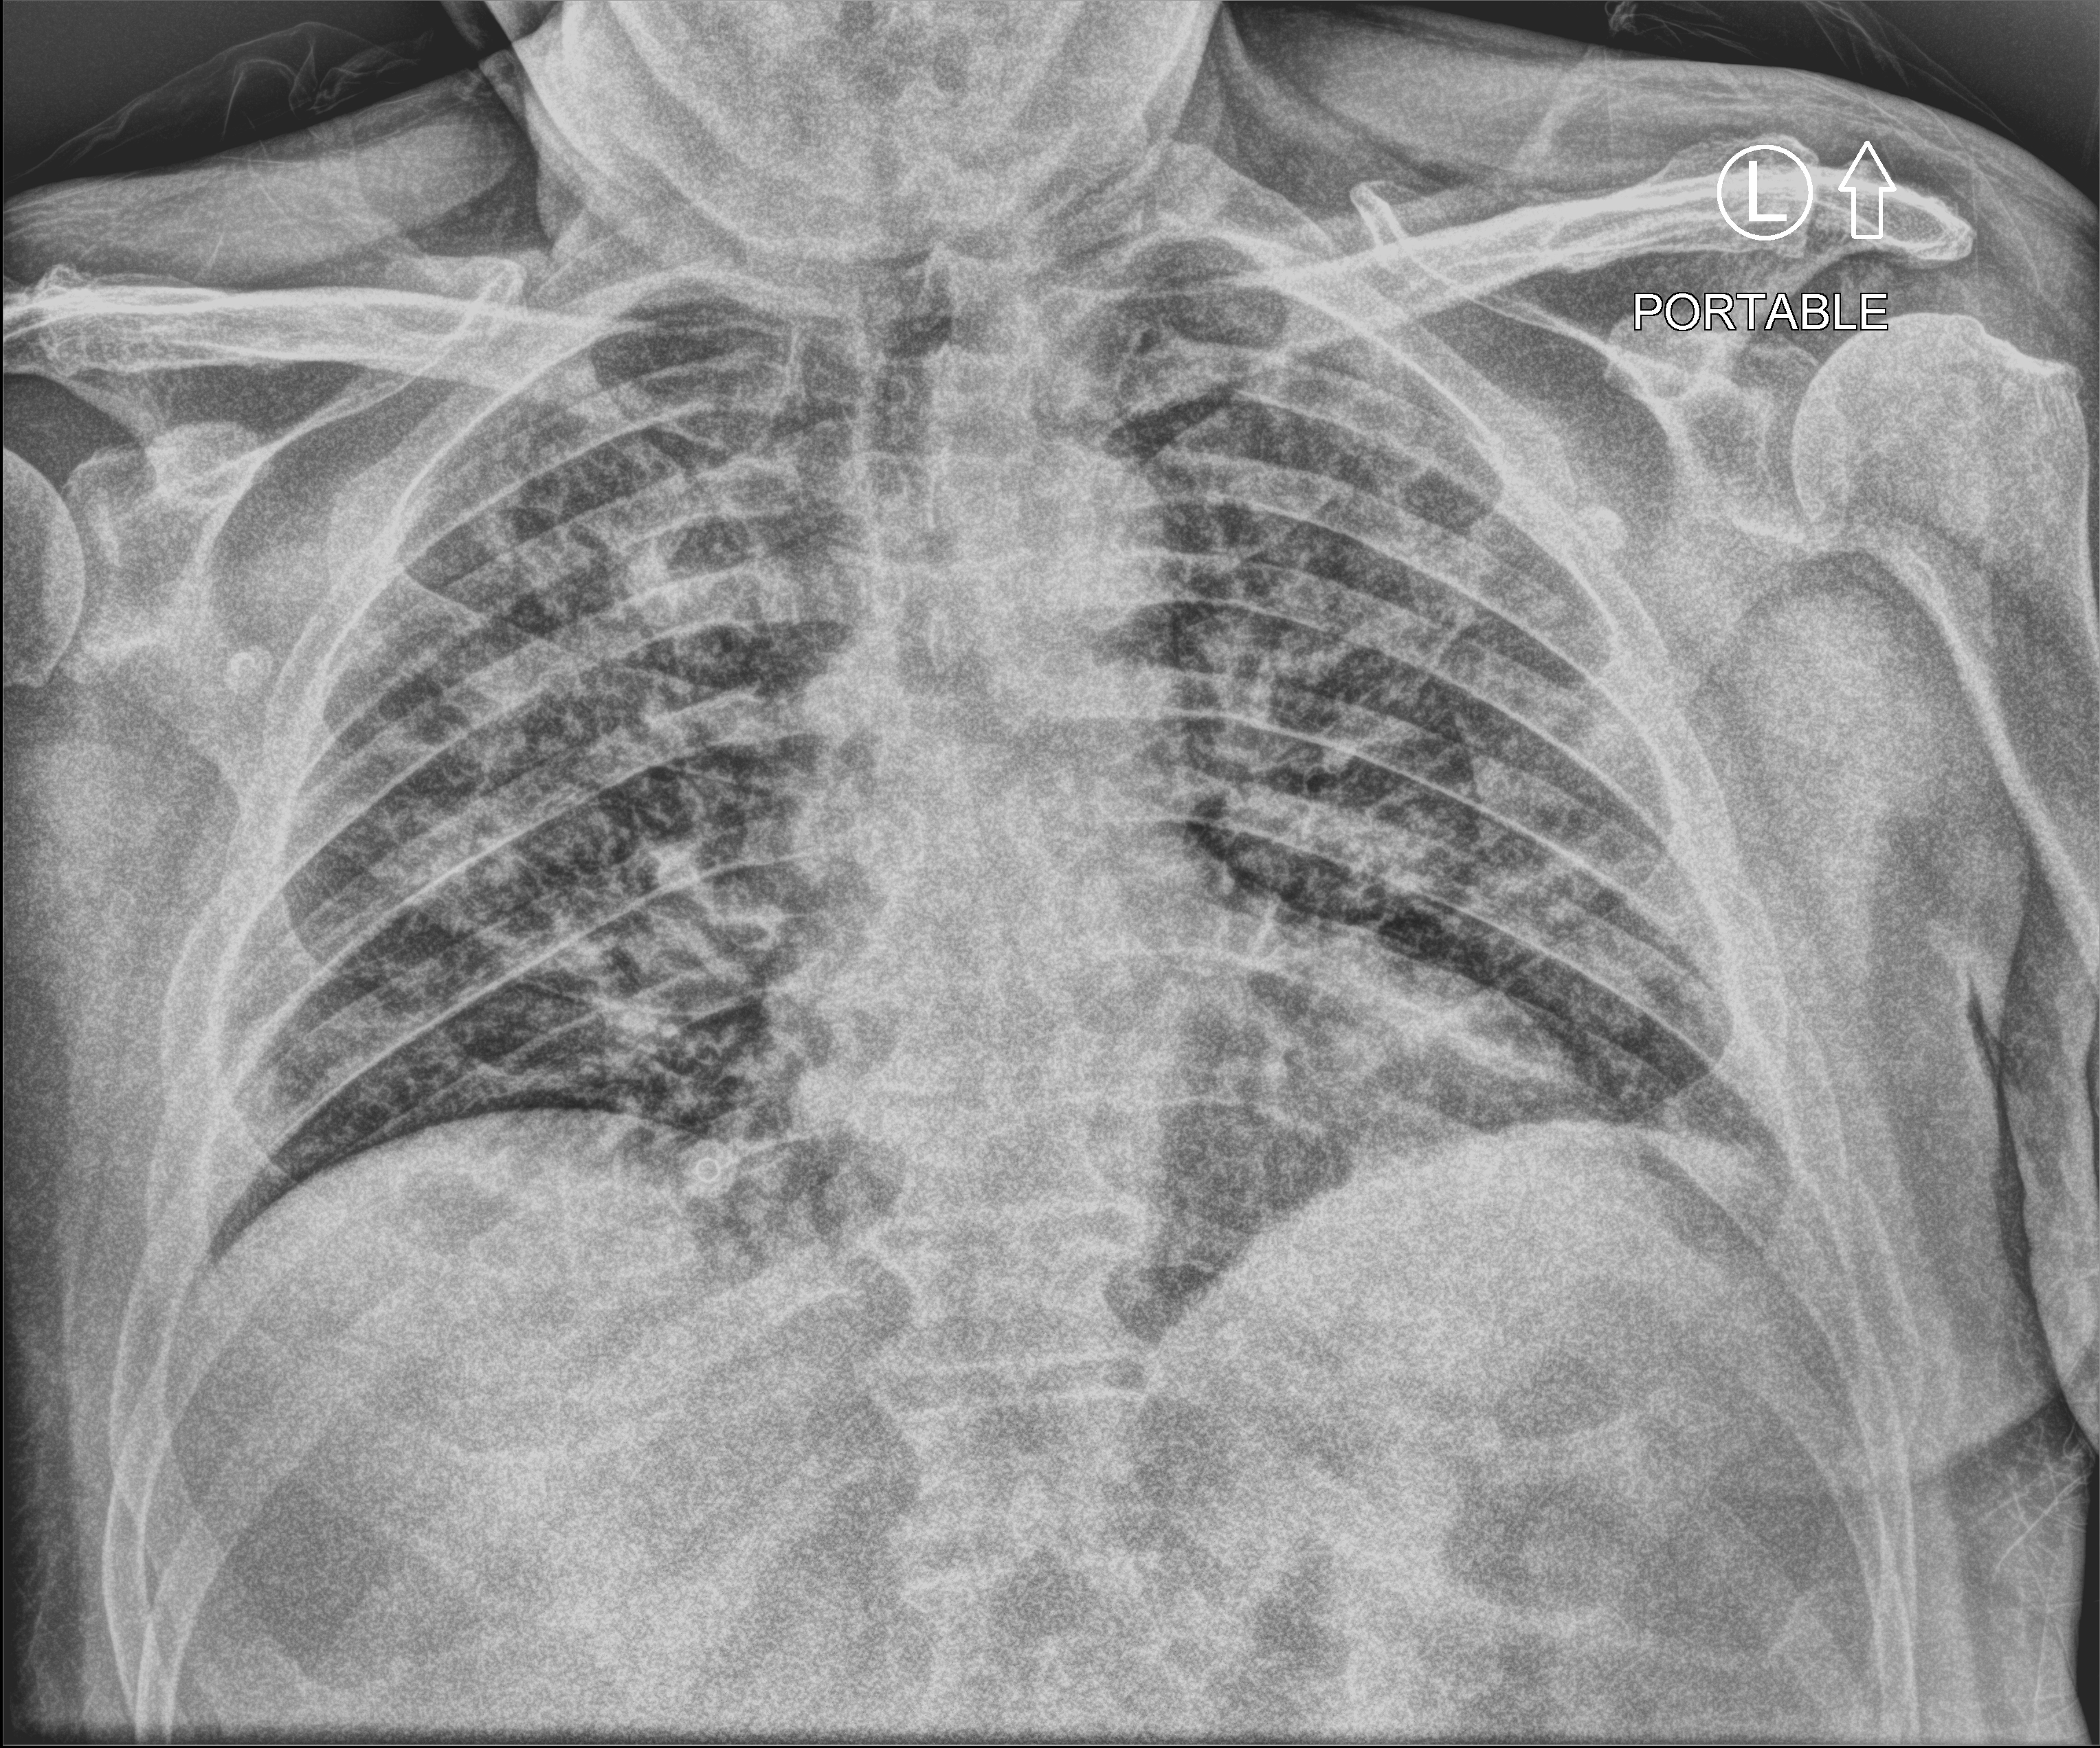
Bedside chest radiograph (computed radiography); anteroposterior (AP) projection. Male patient hospitalised with COVID-19, age 60–74 years.
From the hospital-stay record, not from the radiograph (when in the stay this image was taken is not recorded):
- admitted to intensive care during this hospital stay: no
- mechanically ventilated during this hospital stay: no